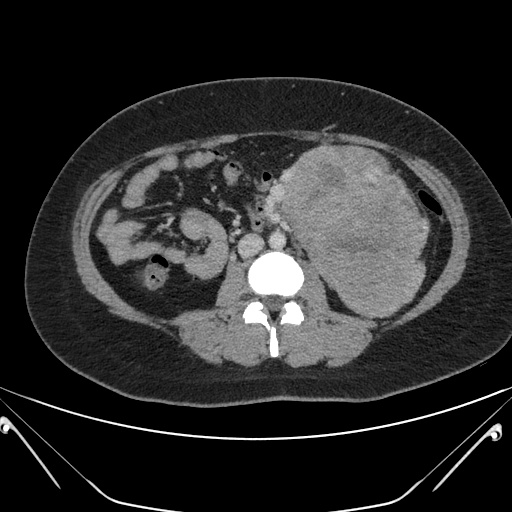
Contrast-enhanced abdominal CT, one axial slice. Position 94 of 168 along the scan axis. Intravenous contrast given. Soft-tissue window (W 400 / L 40 HU). 3 mm slice thickness. 512 × 512 image matrix, field of view 394 × 394 mm. Patient: female, 26 years. From the clinical record (not read from this slice): diagnosis: adrenocortical carcinoma; tumour side: left adrenal; tumour size at pathology: 28 cm; Ki-67 index: 20 %; stage (as recorded): 2.
Outlined on this slice (semi-automatic segmentation, software-assisted and operator-edited):
- mass: box from (x=283, y=147) to (x=425, y=315) px